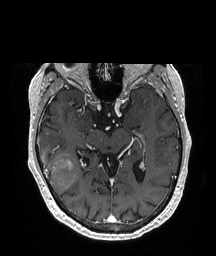
Brain MRI from a brain-tumour surgery series, one axial slice; T1-weighted post-contrast; 216 × 256 image matrix, field of view 216 × 256 mm. From the clinical record (not read from this slice): histopathology: Glioblastoma; WHO grade: 4; IDH mutation: no; tumour location: Right Temporal.
Annotated regions visible in this slice (expert manual segmentation):
- tumour: bounding box <39,149,79,195> (left, top, right, bottom; pixels)